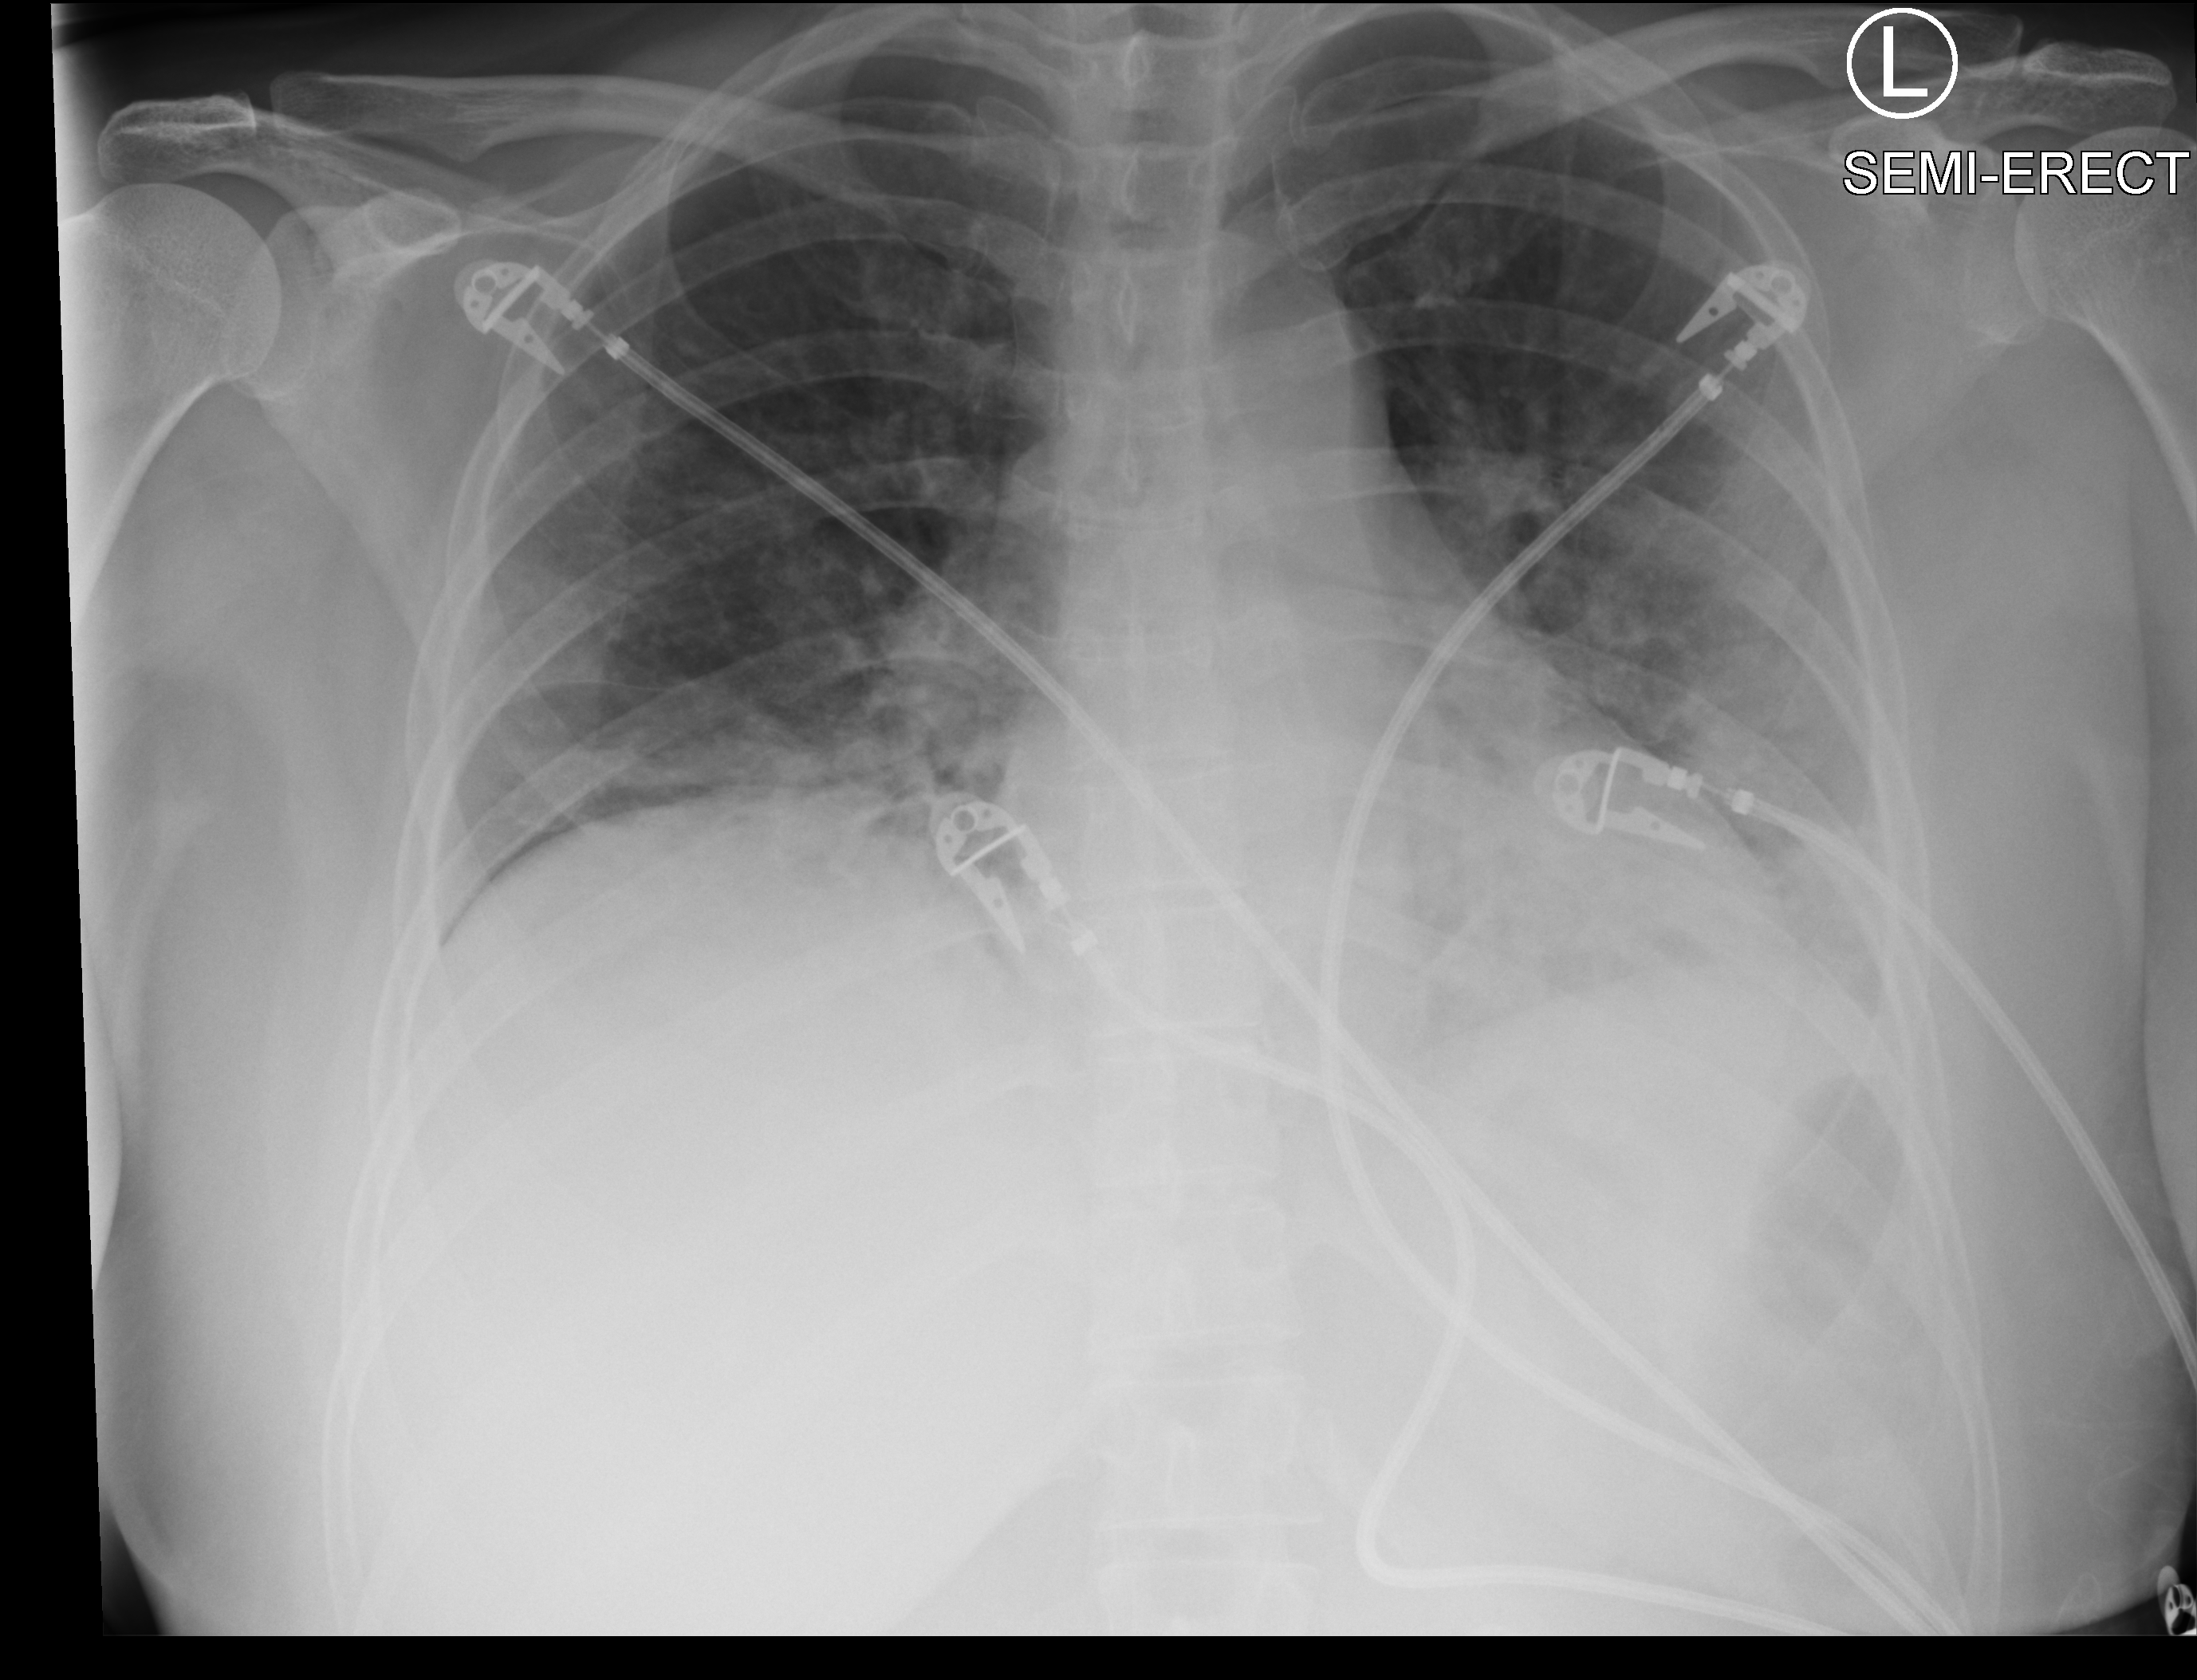
Chest X-ray (portable); anteroposterior (AP) projection. Female patient hospitalised with COVID-19, age 18–59 years.
Hospital-stay facts (about this admission, not read from this image; timing relative to this image not recorded):
- other chronic lung disease (admission record): no